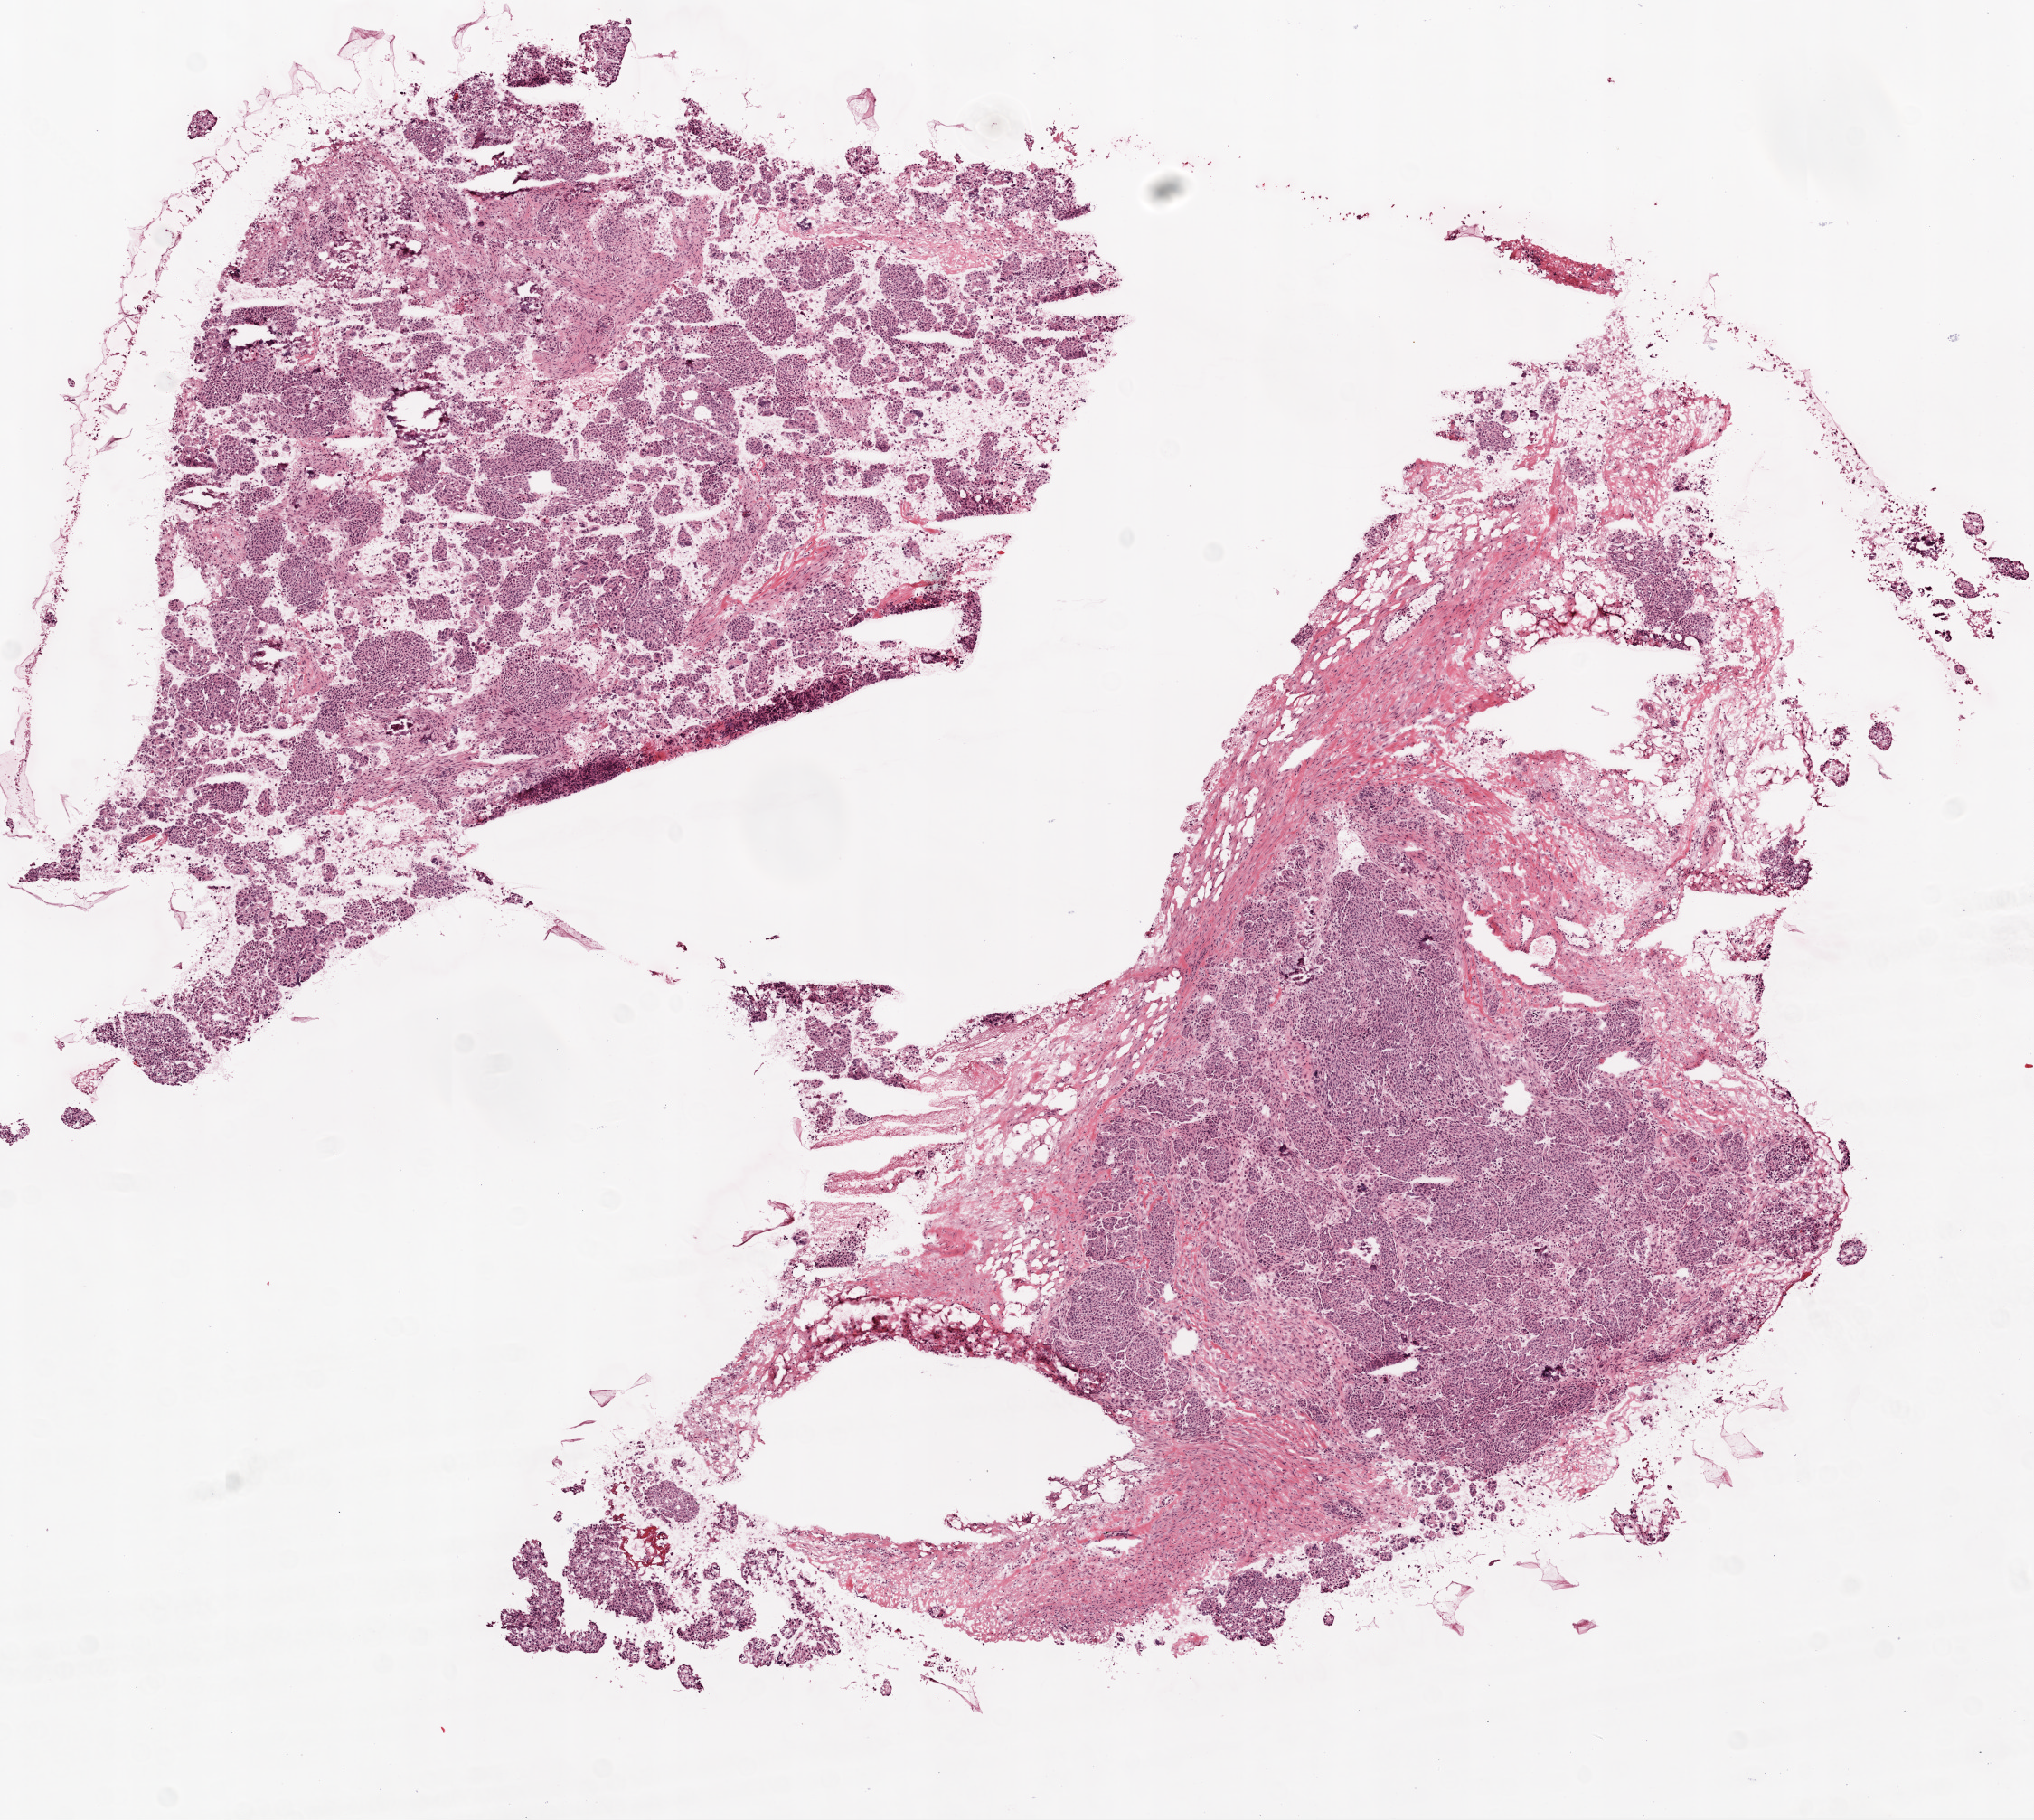
H&E-stained whole-slide image — shown as a low-resolution overview of the whole scanned area (about 9.0 x 8.1 mm). Frozen section from the top of the tissue portion. Primary tumour sample from the ovary. Female, age 72 years at initial diagnosis. Histologic grade: G3 (poorly differentiated). Pathologist review of this section (percent, as recorded): tumour cells 98%, tumour nuclei 85%, normal cells 0%, stromal cells 0%, necrosis 2%.
FIGO stage: IIIC. Pathologic diagnosis: Serous cystadenocarcinoma, NOS.